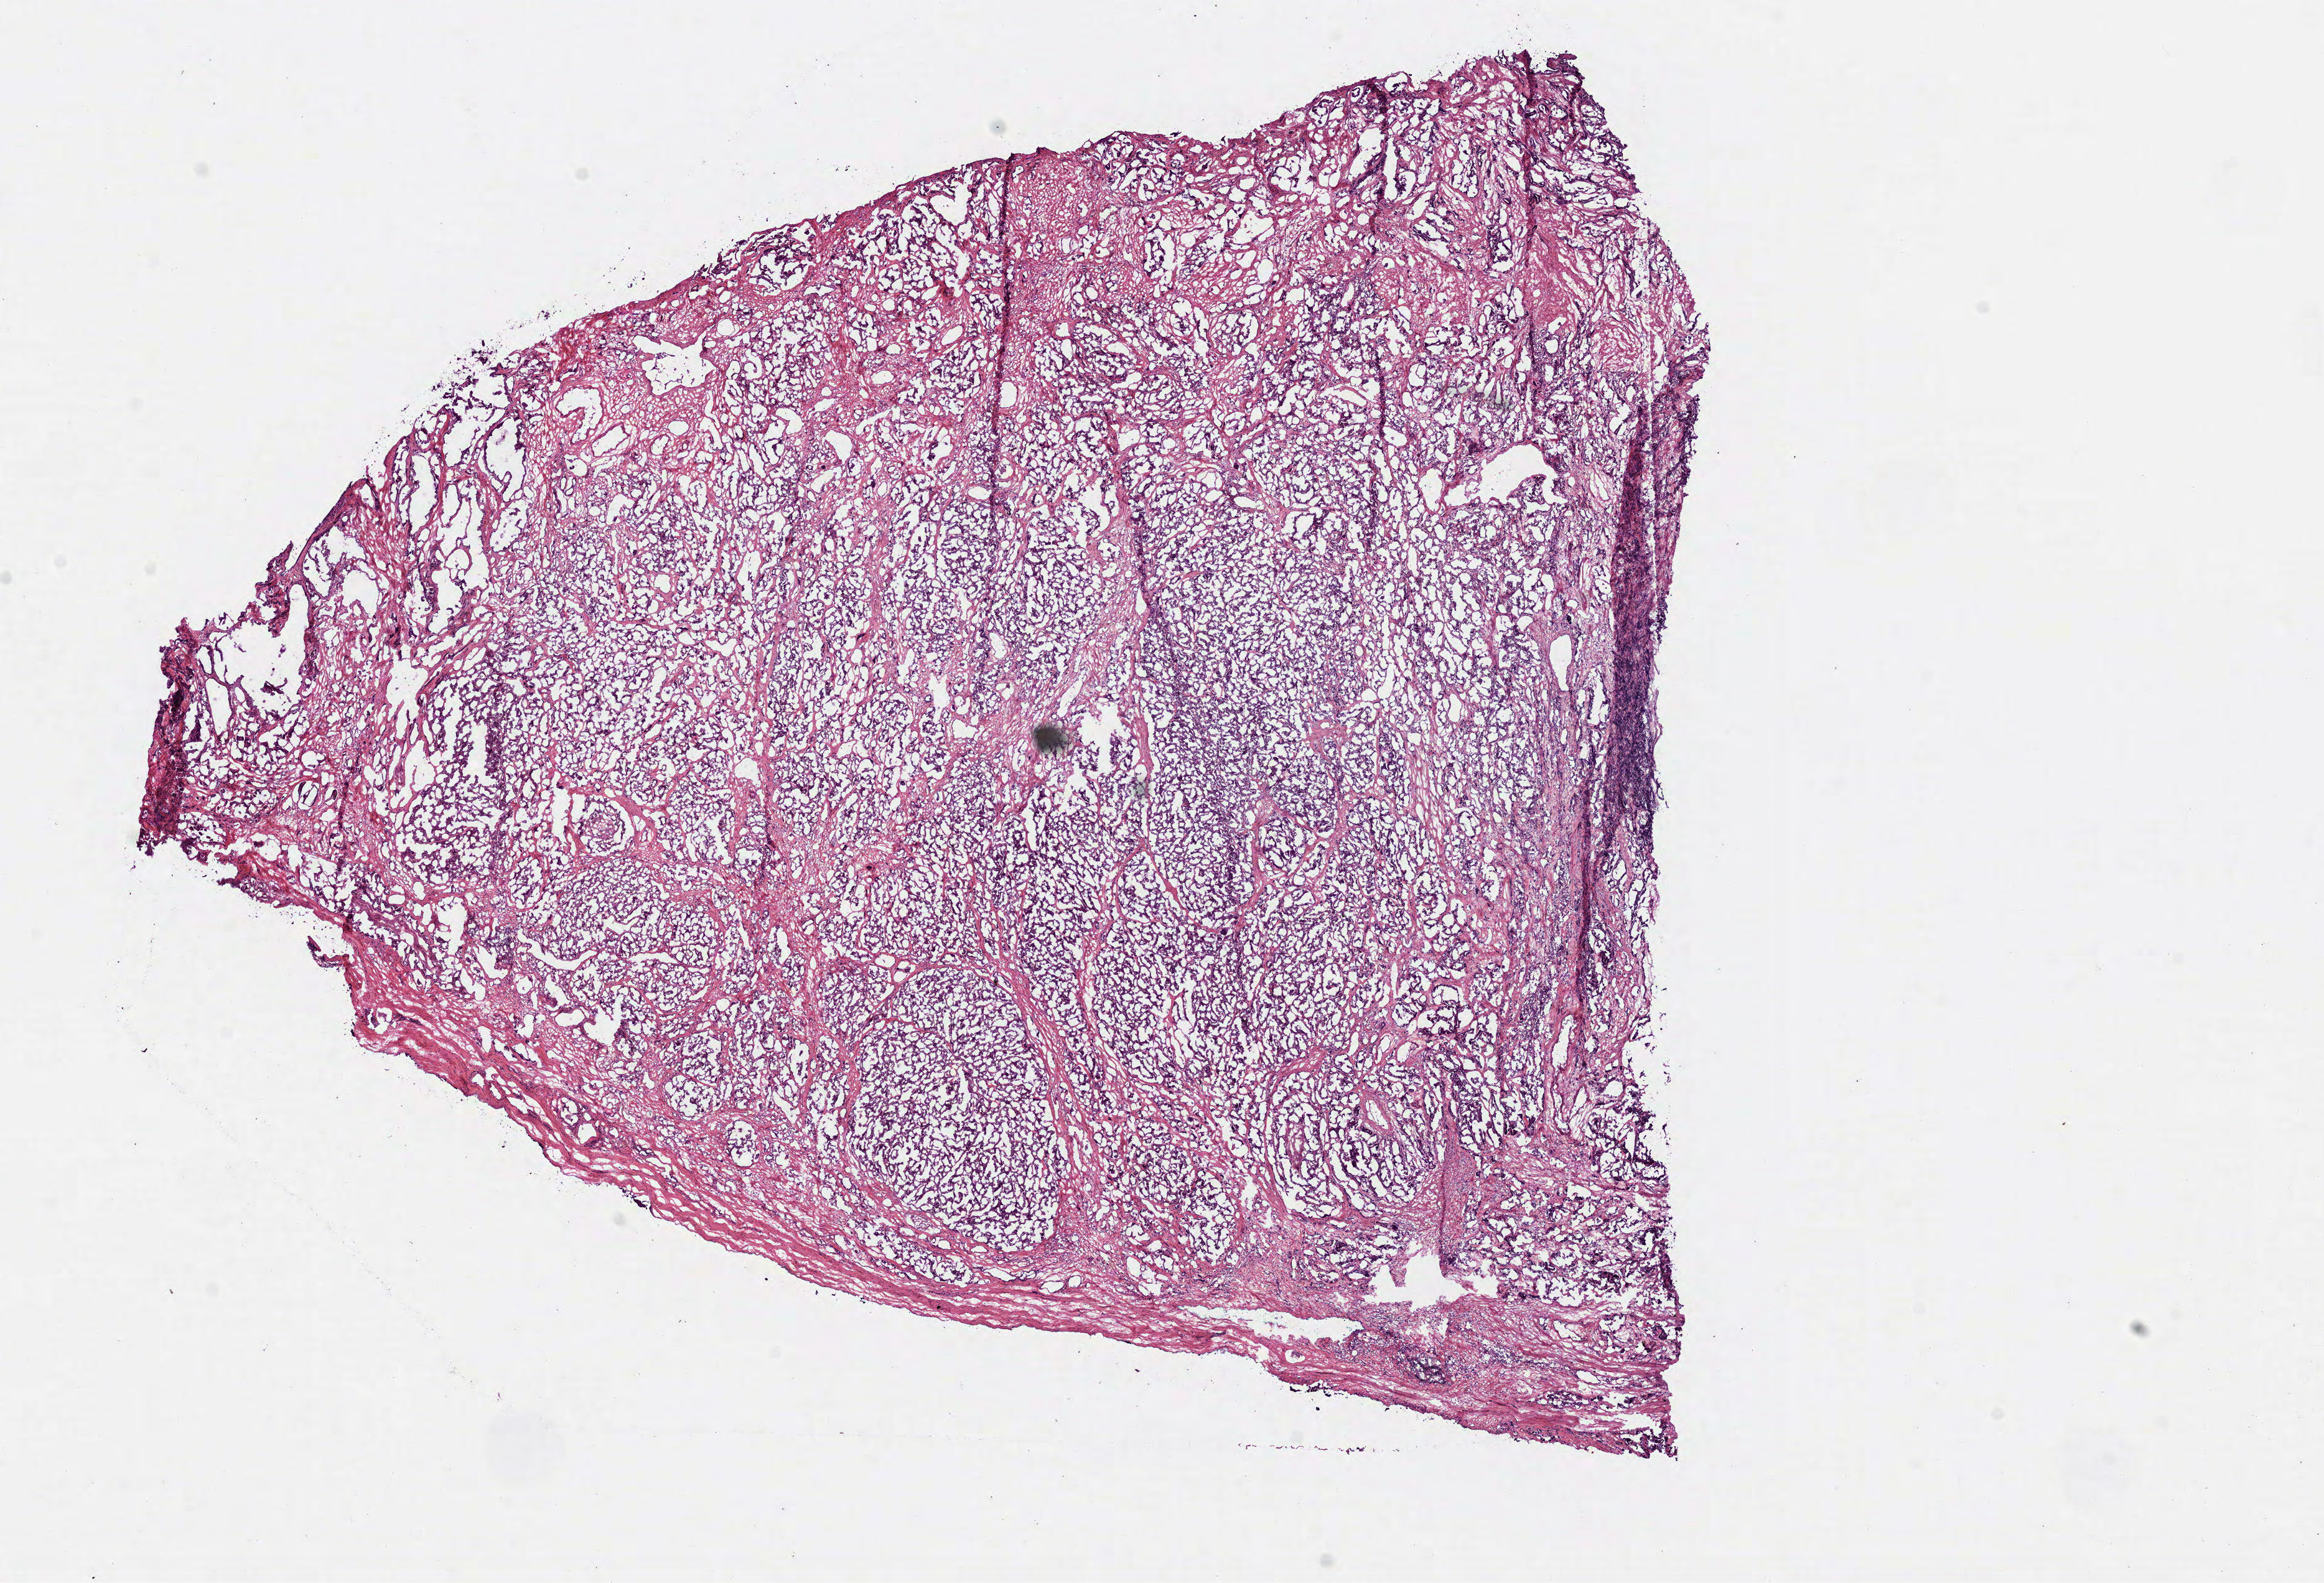
Digitized Hematoxylin and eosin (H&E) stained tissue section (whole slide), a low-resolution overview of the entire scanned area, about 15.1 x 10.3 mm (acquisition: 40x scan); frozen section from the bottom of the tissue portion; sample: primary tumour, prostate. Patient: male, age at initial diagnosis 57 years. Gleason score: 7 (4+3). Pathologist review of this section (percent, as recorded): tumour cells 75%, tumour nuclei 75%, normal cells 5%, stromal cells 20%, necrosis 0%. Inflammatory infiltration, as recorded: lymphocyte infiltration 5%, monocyte infiltration 0%, neutrophil infiltration 0%.
• histologic diagnosis: Acinar cell carcinoma (prostate gland)